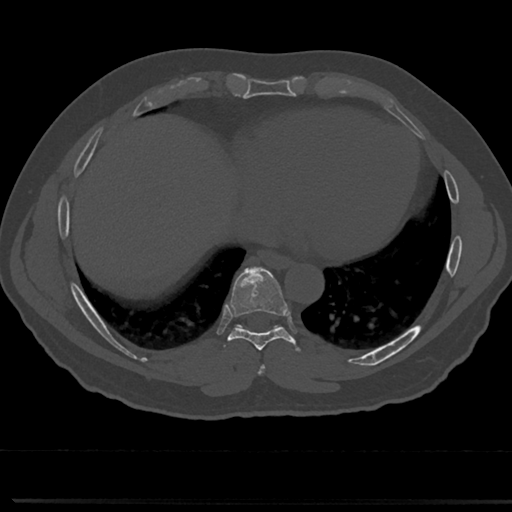
CT including the spine, one axial slice; position 347 of 817 along the scan axis; reconstruction kernel Br40s/3; 120 kVp; bone window (W 1800 / L 400 HU); 0.5 mm slice thickness; 512 × 512 image matrix, field of view 355 × 355 mm. Male patient, age 61 years. Case-level facts recorded for this patient, not image findings: primary cancer: prostate.
Structures marked on this image (semi-automatically segmented with operator editing):
- T7 vertebra: bounding box [x1, y1, x2, y2] px = [255, 340, 269, 376]
- T8 vertebra: [218, 271, 302, 352]